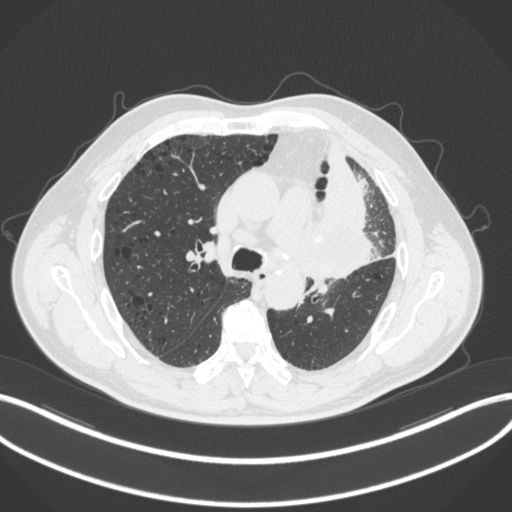
Chest CT, one axial slice. Position 187 of 286 along the scan axis. 120 kVp. Lung window (W 1500 / L -600 HU). 512 × 512 image matrix, field of view 400 × 400 mm. Male patient, age 68 years. From the clinical record (not read from this slice): clinical TNM (as recorded): T3 N3 M1.
Annotated regions visible in this slice (rectangle marked by the reading radiologist):
- lung tumour (recorded histology: adenocarcinoma): box from (x=308, y=164) to (x=386, y=287) px